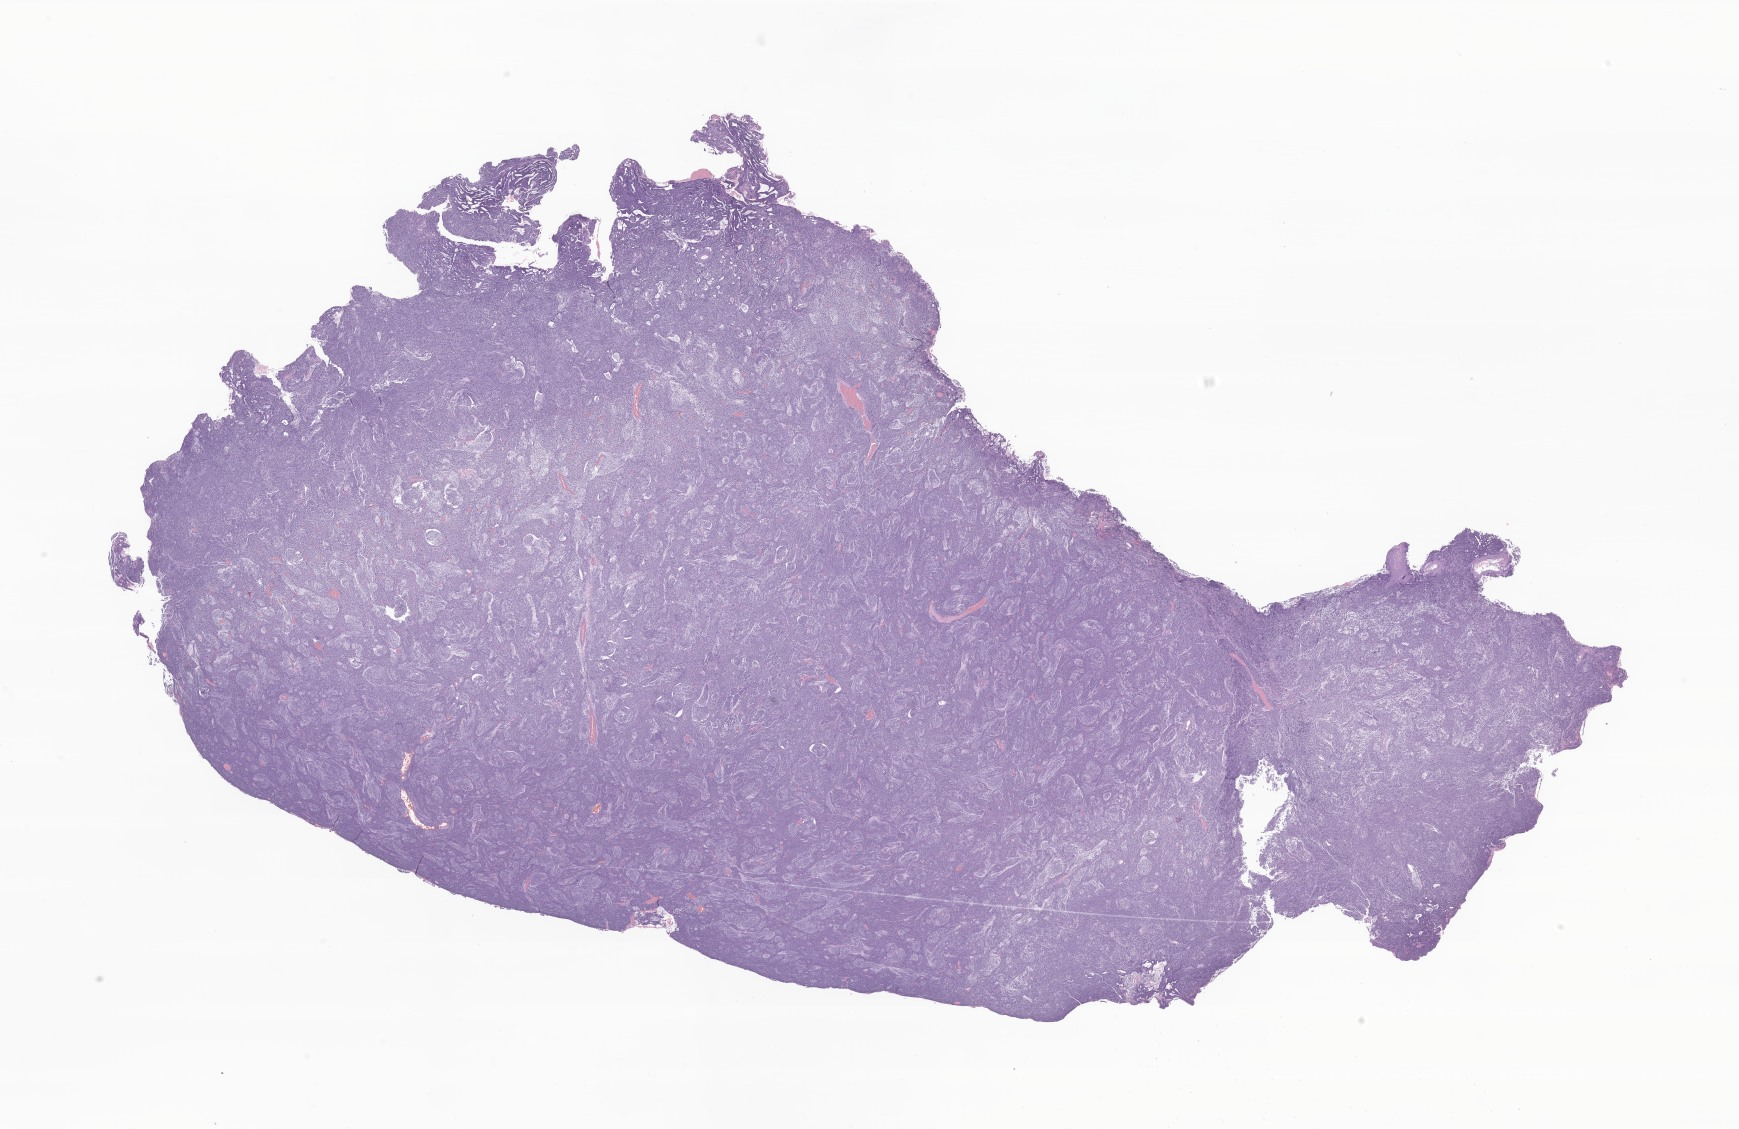
H&E whole-slide image of tumor tissue from the cerebellum — shown as a low-resolution overview of the whole scanned area (about 29.3 x 19.0 mm). FFPE section. Patient male; age 912 days (about 2.5 years).
Recorded diagnosis: Medulloblastoma, NOS.